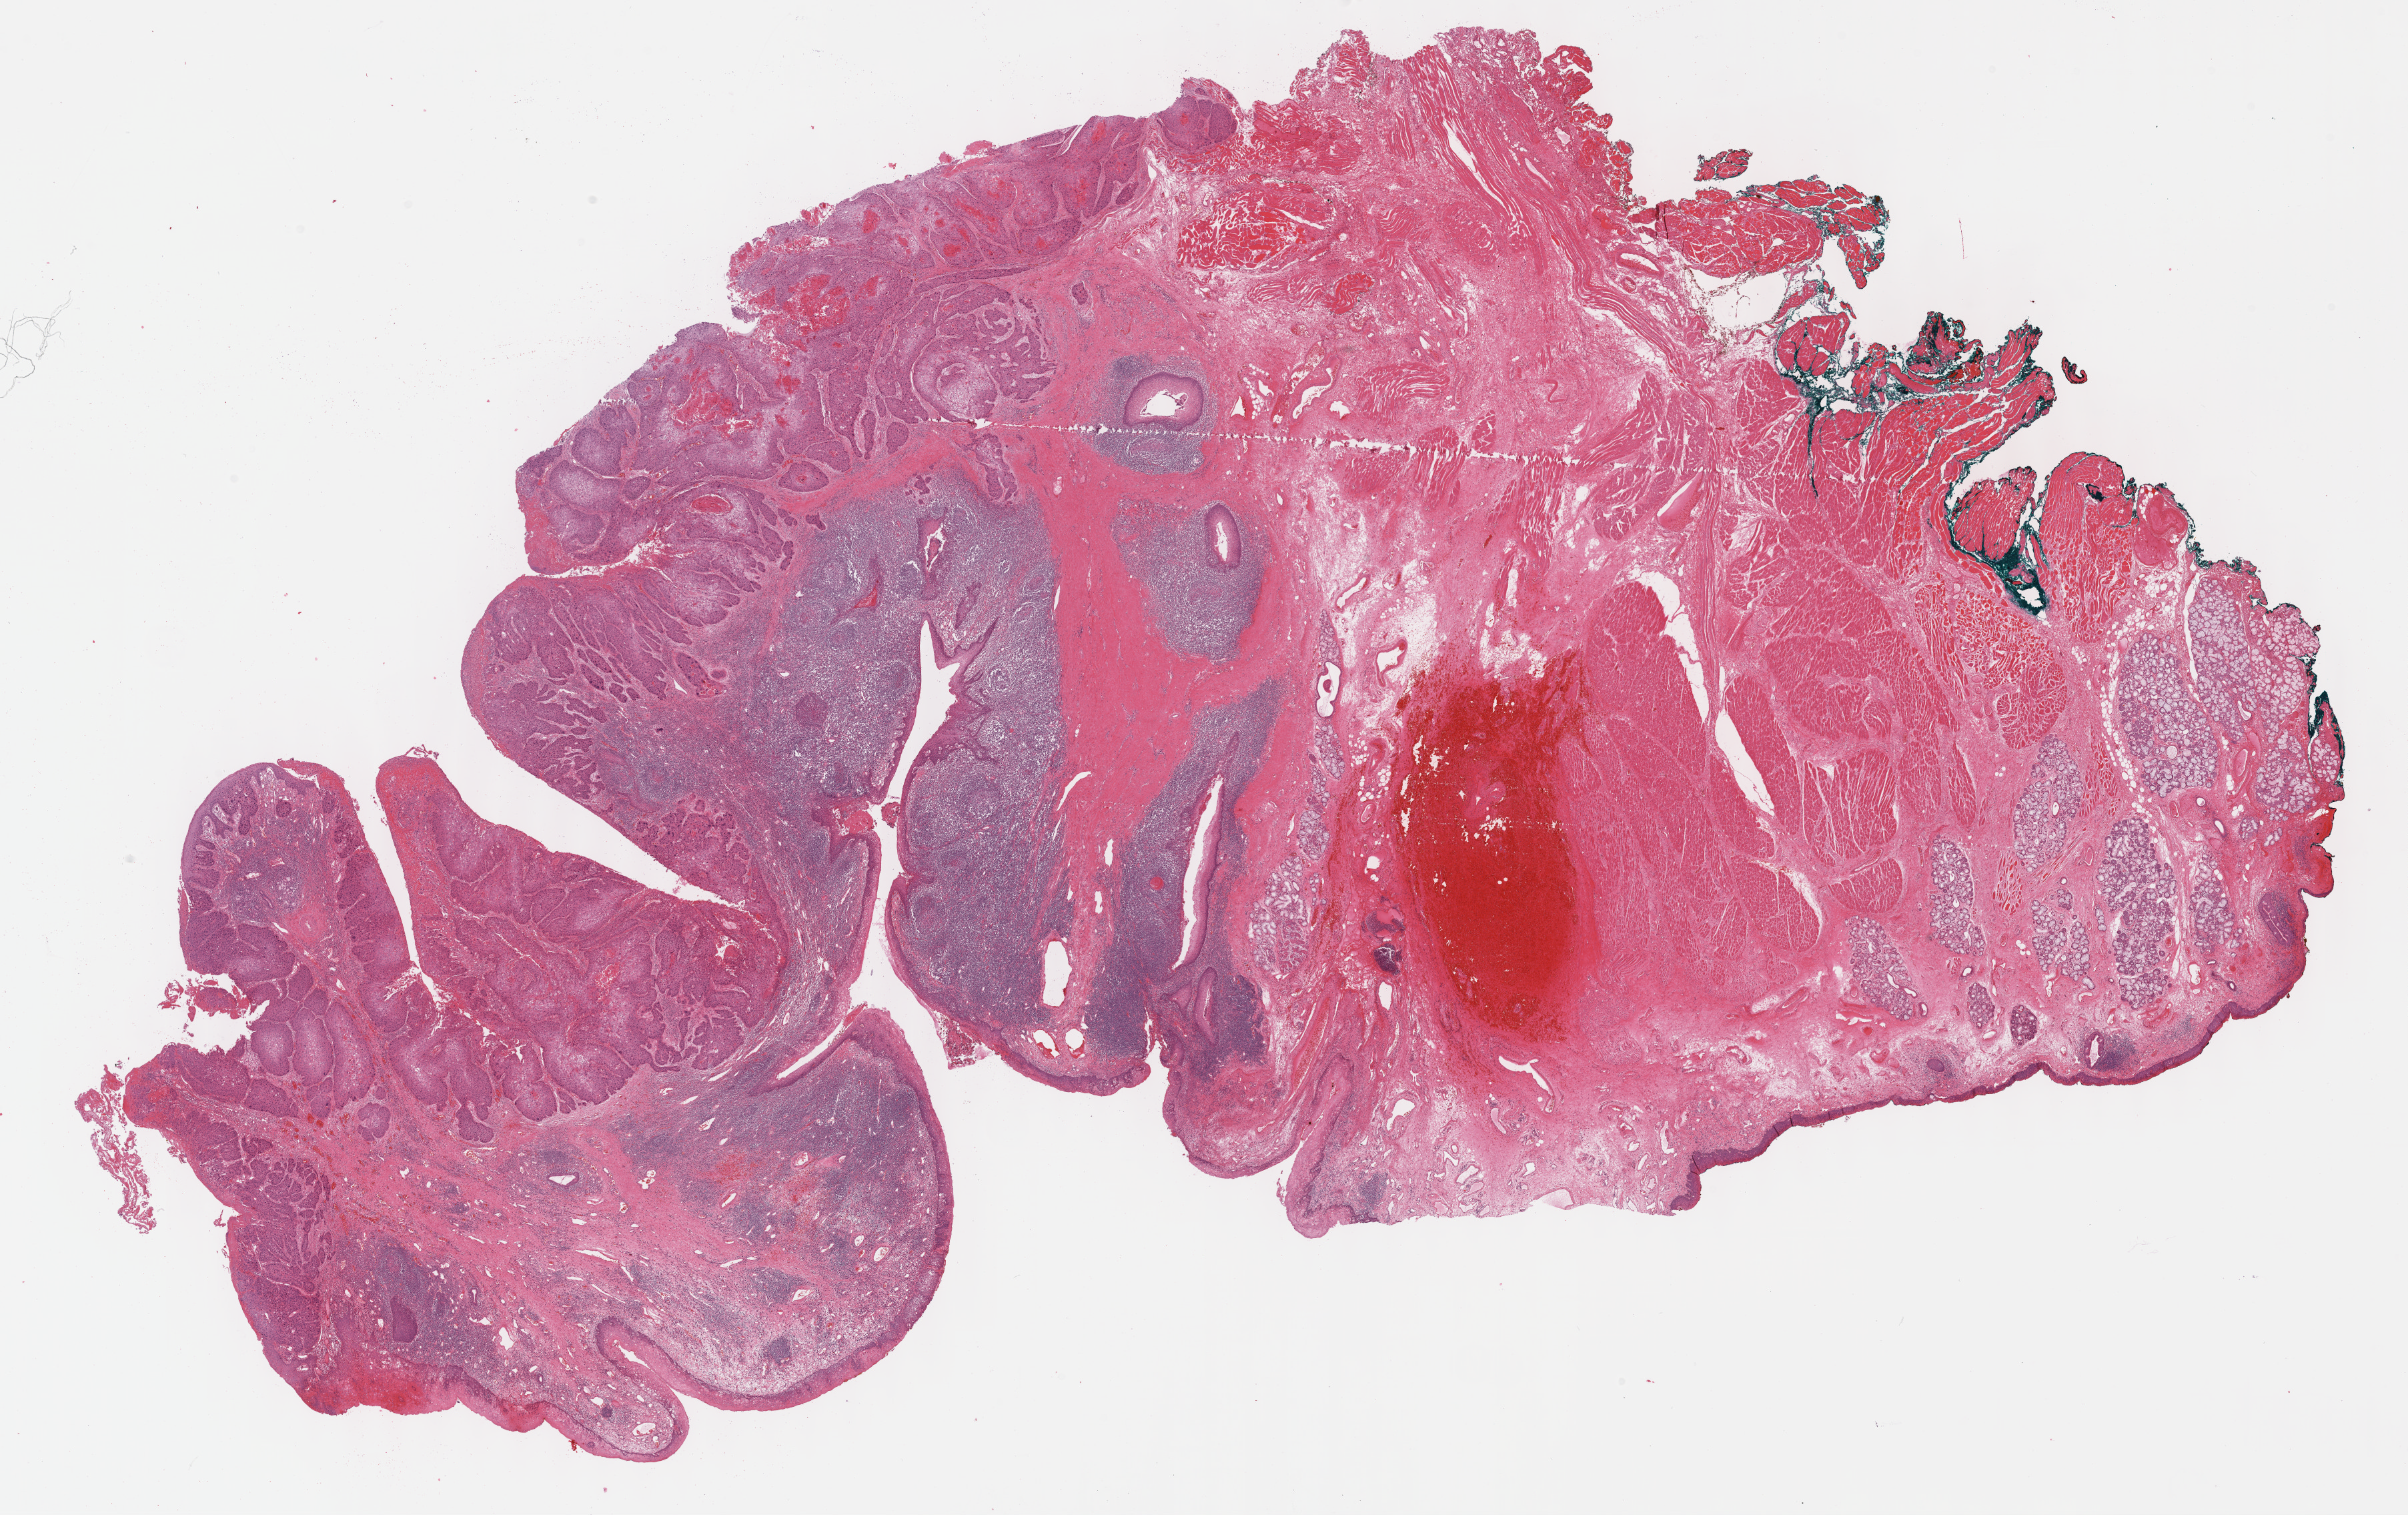
Digitized H&E-stained tissue section (whole slide) — shown as a low-resolution overview of the whole scanned area (about 29.2 x 18.4 mm); formalin-fixed paraffin-embedded (FFPE) diagnostic section; head and neck, primary tumour sample. Male patient; age at initial diagnosis 53 years. Histologic grade: G2 (moderately differentiated).
- laterality: left
- diagnosis: Squamous cell carcinoma, NOS (base of tongue, NOS)